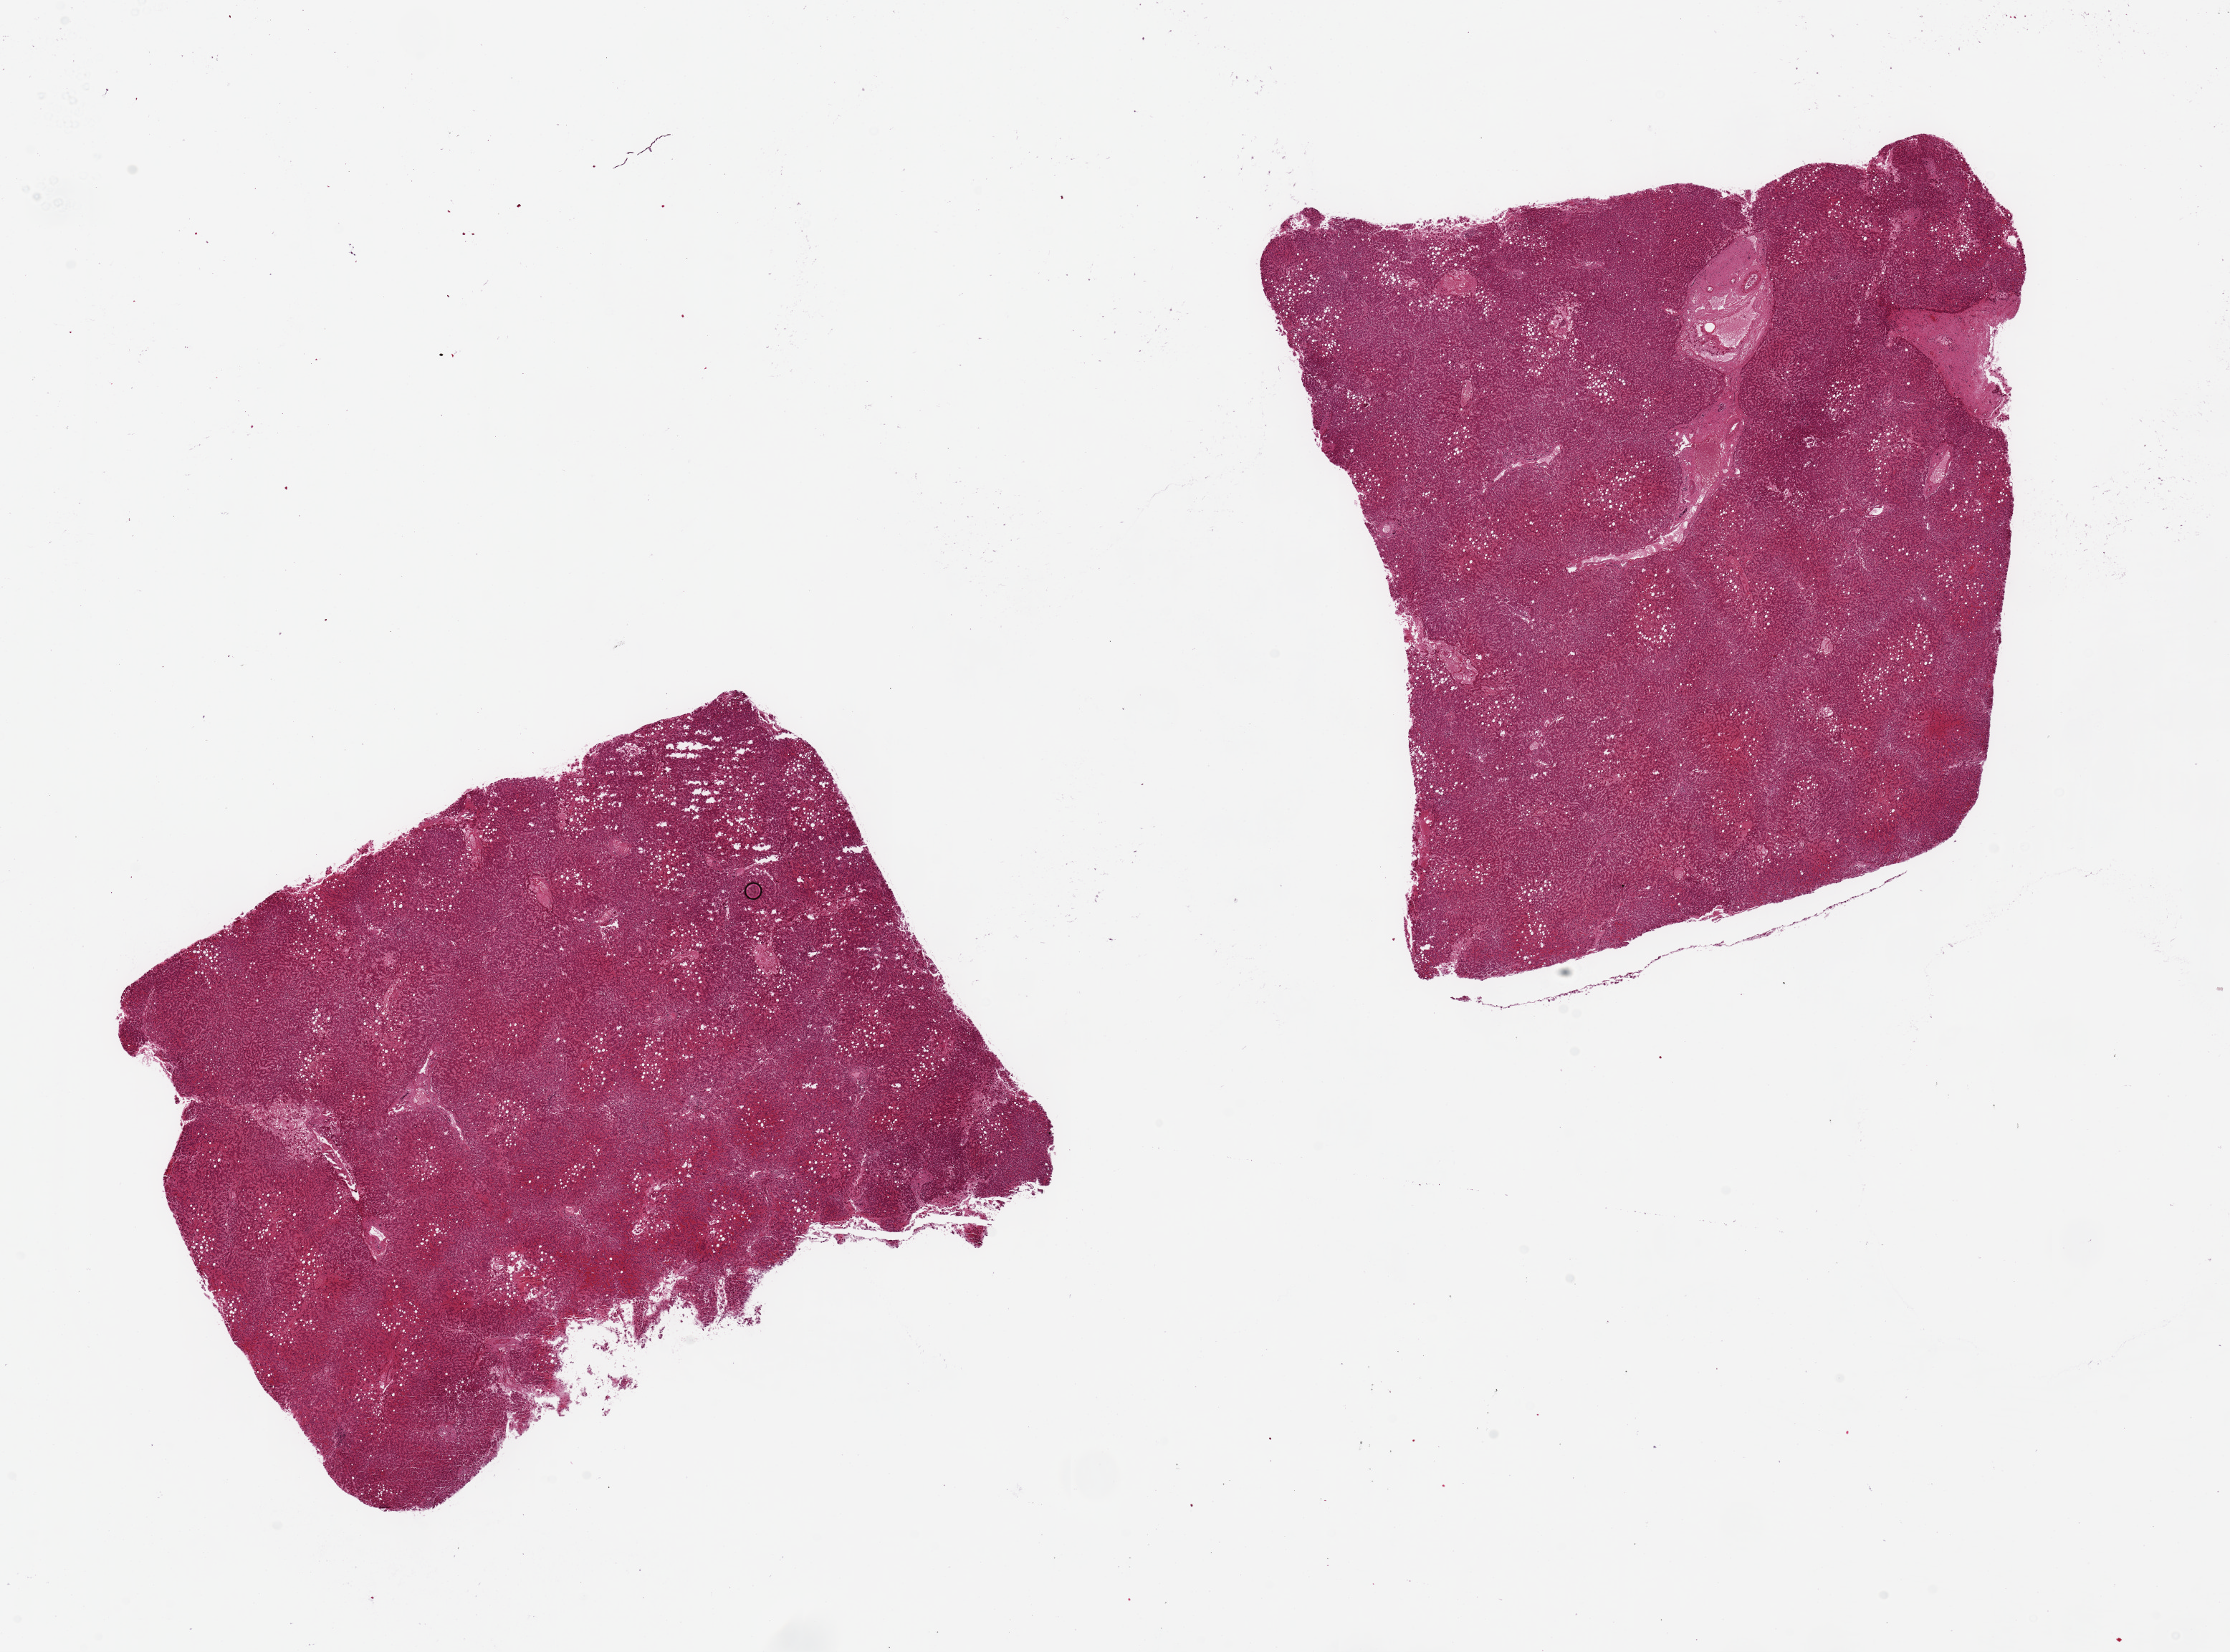
Hematoxylin and eosin (H&E) whole-slide image — low-resolution overview of the scanned area, about 24.6 x 18.2 mm (acquisition: 20x scan); PAXgene-fixed paraffin-embedded (PFPE) section; target tissue: liver; tissue donor sample. Donor sex: female.
* reviewer comment on this tissue sample: 2 pieces, 8x8 & 9x7mm; moderately congested centrally associated with macrovesicular steatosis